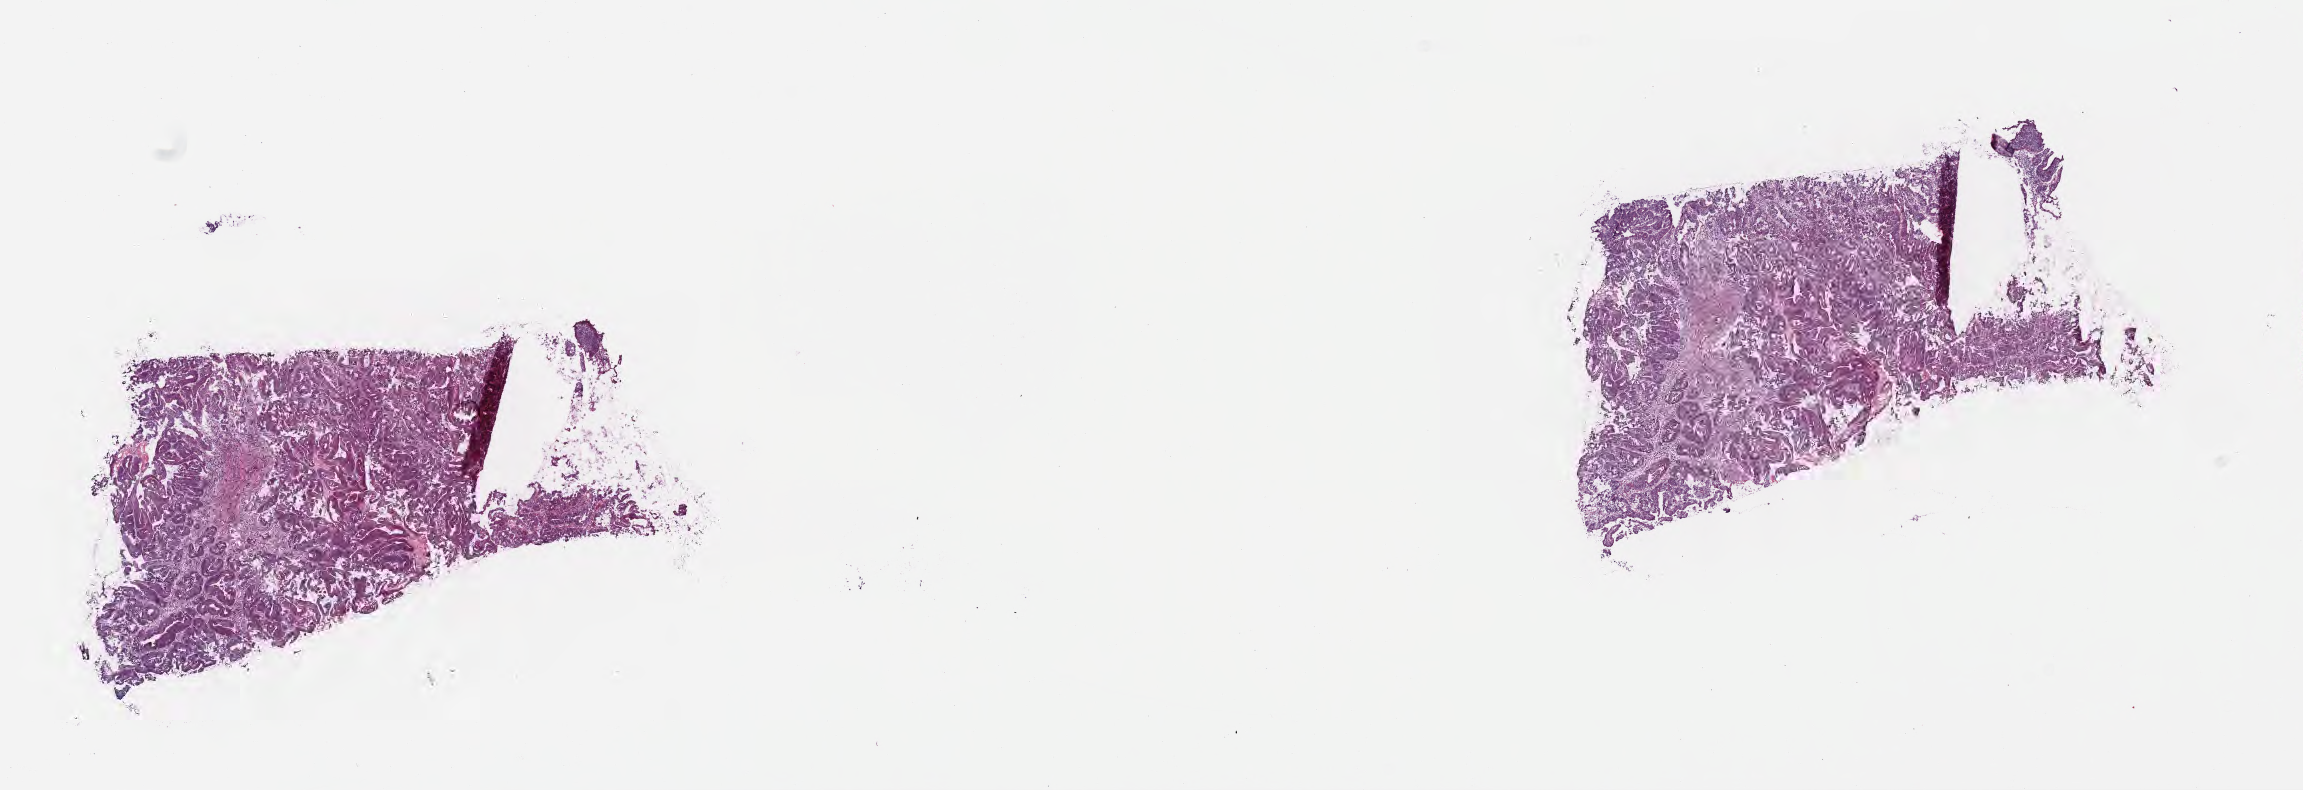
Digitized hematoxylin and eosin (H&E)-stained section — whole scanned area (about 18.6 x 6.4 mm) shown as a low-resolution overview; frozen section; specimen: primary tumor; site: rectosigmoid junction. Female, age 70 years at initial diagnosis. Tumor grade: G2 (moderately differentiated). Pathologist review of this section (percent, as recorded): tumor cells 80%, tumor nuclei 80%, stromal cells 20%, necrosis 0%, normal cells 0%. Inflammatory infiltration, as recorded: lymphocyte infiltration 6%, monocyte infiltration 2%, neutrophil infiltration 7%.
AJCC pathologic stage: Stage I. Histologic diagnosis: Adenocarcinoma, NOS. Section: top of the tissue portion.